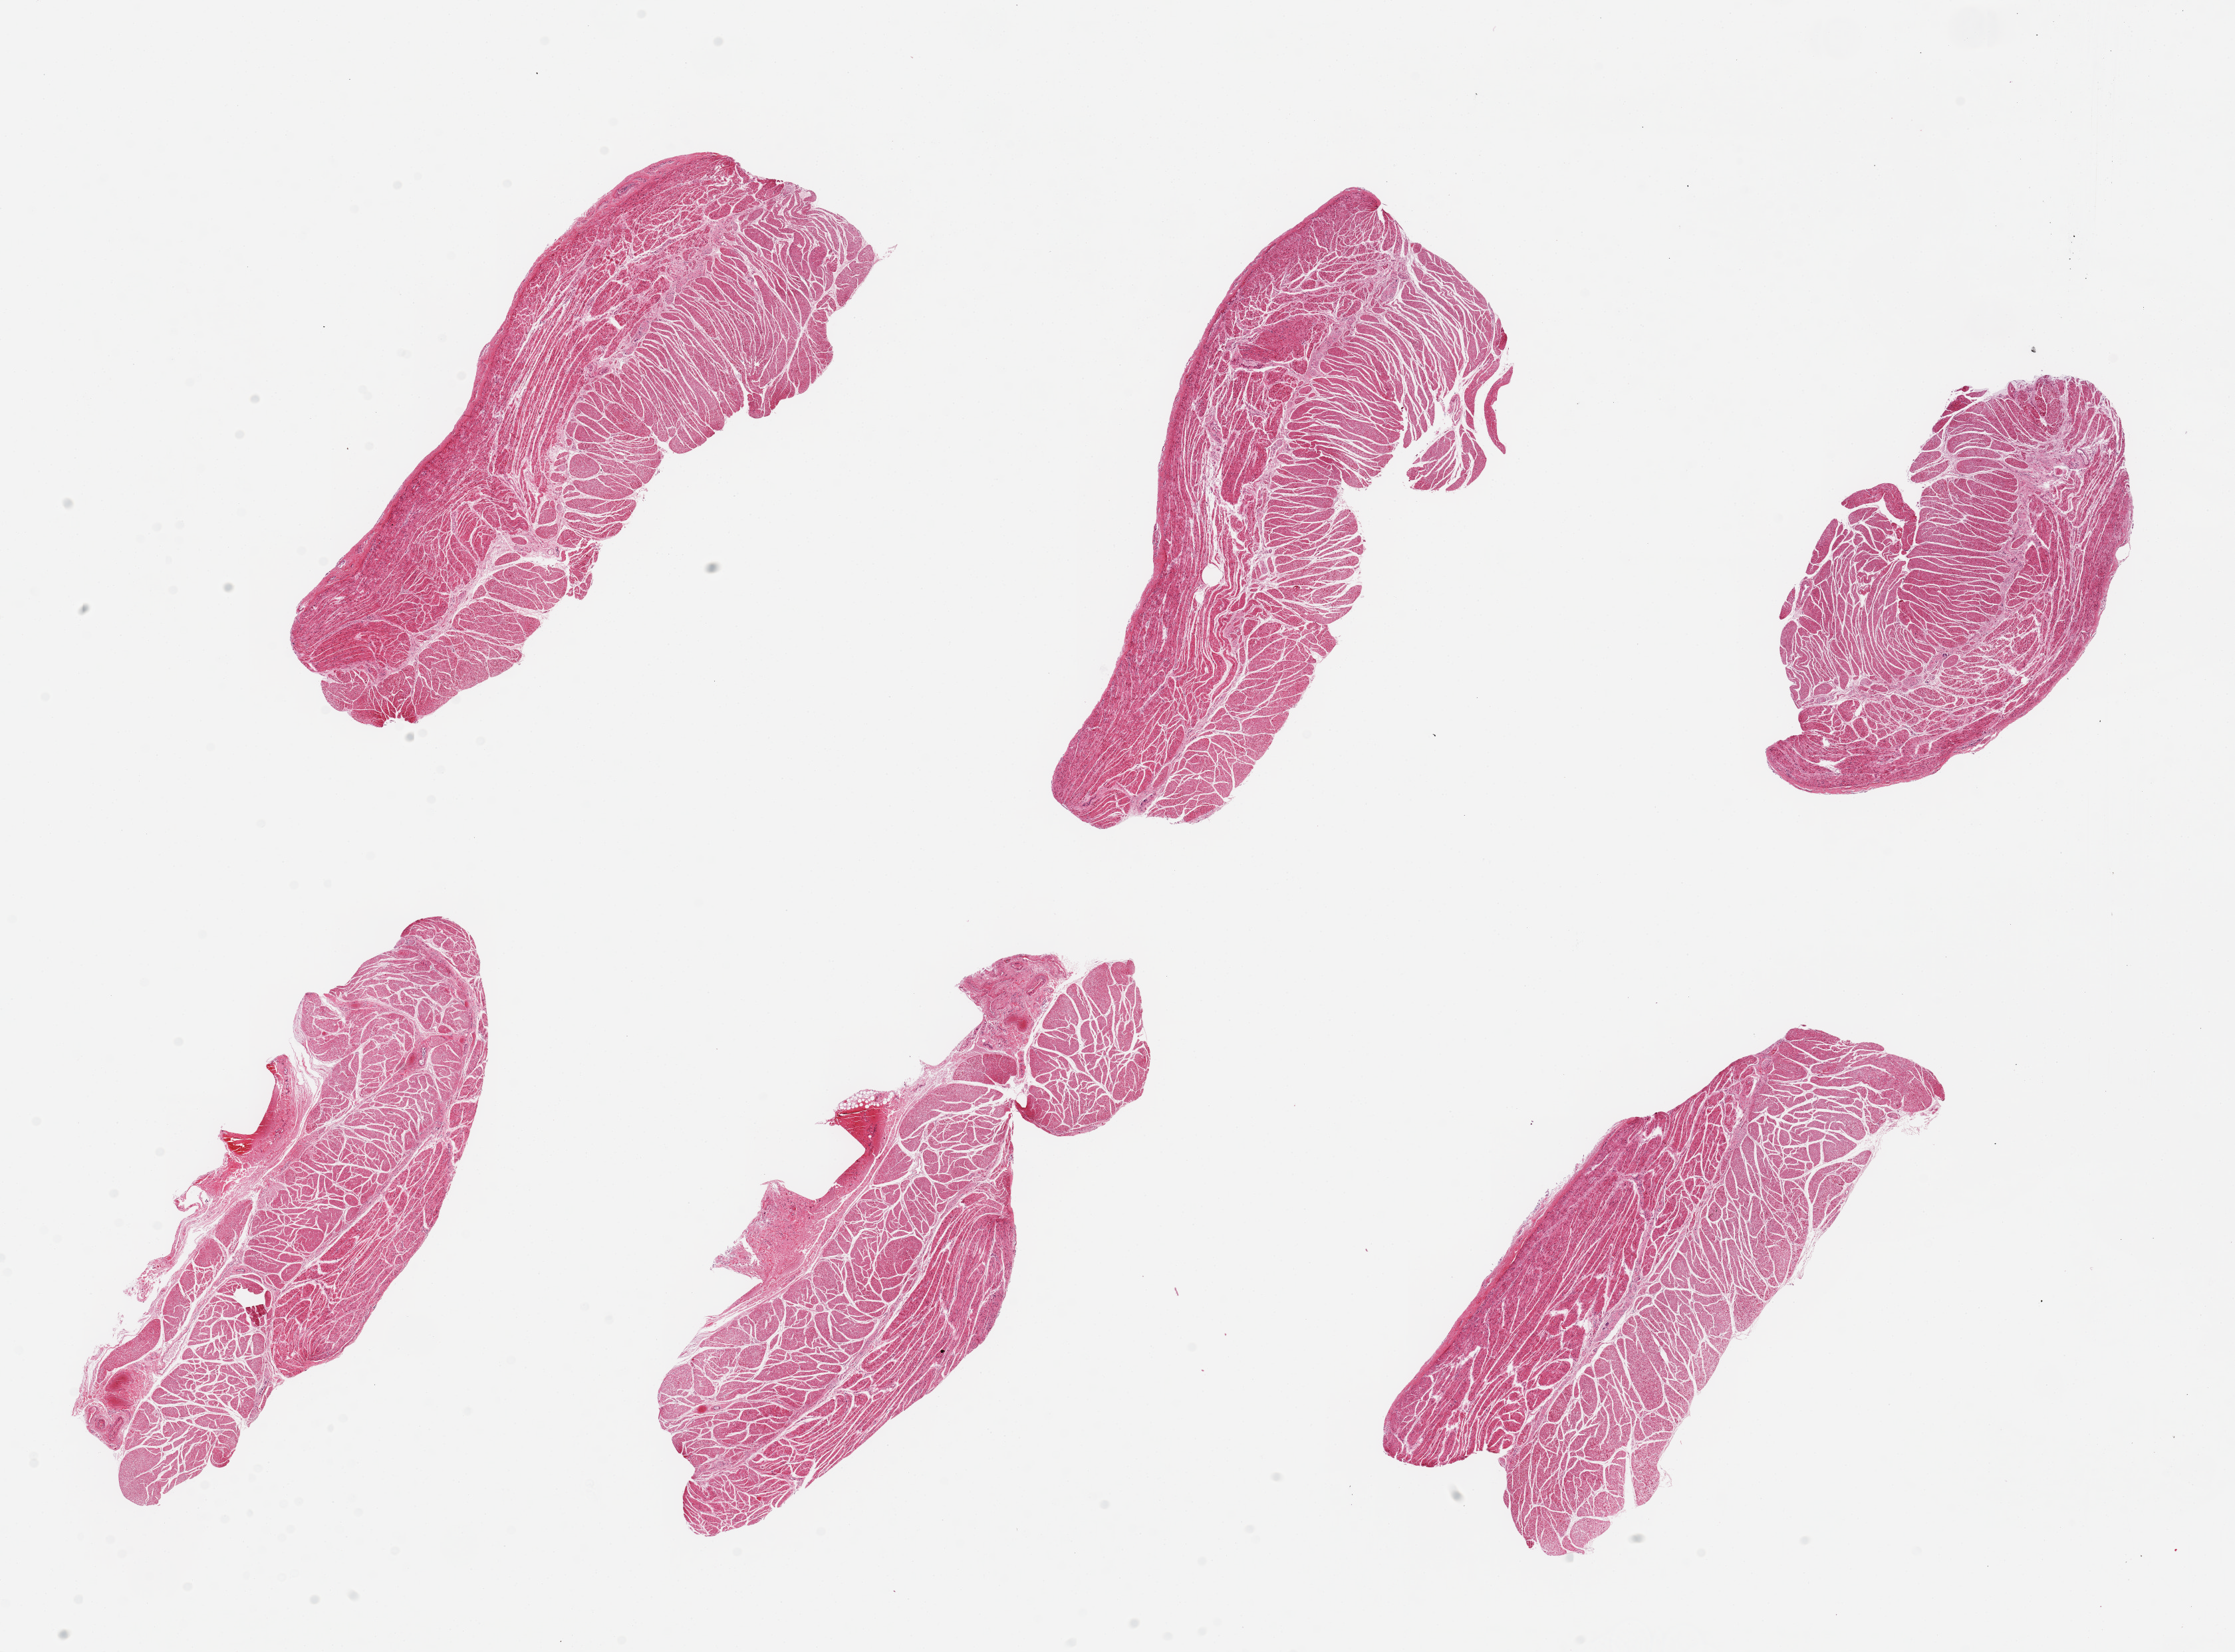
Digitized haematoxylin and eosin-stained section, low-resolution overview of the scanned area, about 26.6 x 19.7 mm. PAXgene-fixed, paraffin-embedded tissue. Target tissue: esophageal muscle. Tissue donor sample.
• review note (as recorded): 6 pieces, up to 8x4mm; well trimmed muscularis